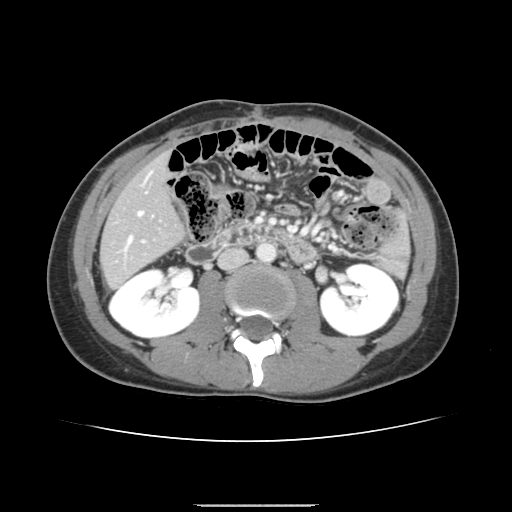
Contrast-enhanced abdominal CT, one axial slice. Slice 56 of 150 in the series (ordered by position). 120 kVp. Intravenous contrast given. Soft-tissue window (W 400 / L 40 HU). 512 × 512 image matrix, field of view 324 × 324 mm. Female patient, age 32 years. From the clinical record (not read from this slice): diagnosis: colorectal cancer liver metastases, imaged before liver resection; multiple liver metastases: yes; largest metastasis: 0.7 cm; disease in both lobes: no.
Structures marked on this image (expert manual segmentation):
- hepatic veins: bounding box (x1, y1, x2, y2) in pixels: (125, 211, 143, 250)
- liver: (101, 156, 184, 287)
- planned liver remnant (the part of the liver to remain after resection): (101, 156, 183, 287)
- portal vein (with intrahepatic branches): (125, 172, 151, 253)